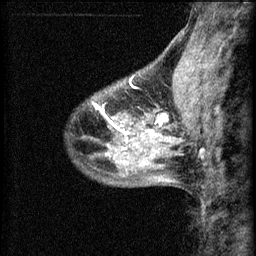
Breast MRI (dynamic contrast-enhanced), one sagittal slice; position 21 of 60 along the scan axis; 3 images stored at this slice position (order not interpretable as contrast timing); 1.5 T; TE 4.2 ms, TR 8.2 ms; 256 × 256 image matrix, field of view 180 × 180 mm. Patient: female, 40 years.
Annotated regions visible in this slice (semi-automatic segmentation, software-assisted and operator-edited):
- analysis volume of interest (the breast-tissue region the enhancement analysis was run in; not a lesion): bounding box [x1, y1, x2, y2] px = [108, 82, 175, 139]
- tumour enhancement mask (voxels above the 70 % enhancement threshold inside the analysis volume of interest): [108, 114, 169, 135]